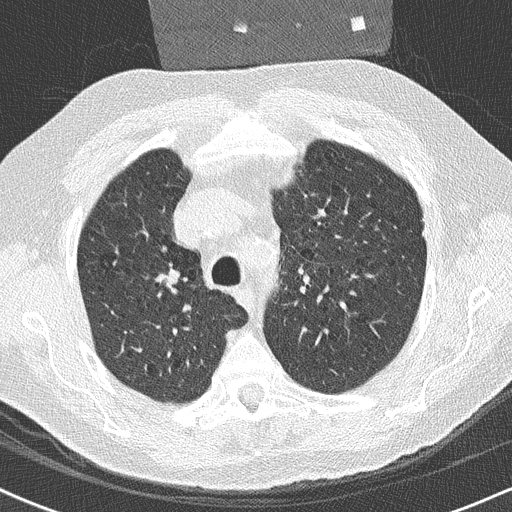
Chest CT (low-dose screening protocol), one axial image; baseline annual screen; lung window (W 1500 / L -600 HU); 2 mm slice thickness; 120 kVp; 512 × 512 image matrix, field of view 314 × 314 mm. Male, age 59 years at enrolment. Former smoker at enrolment.
- Lesion marked by an expert reader, box from (x=145, y=260) to (x=189, y=300) px.
- No non-calcified nodule or mass ≥4 mm was recorded by the screening reader at this exam.
- Official screen result: negative screen, minor abnormalities not suspicious for lung cancer.
- Participant outcome: lung cancer diagnosed 360 days after this screen (after the second annual screen) — squamous cell carcinoma, NOS, right upper lobe, poorly differentiated (G3), stage IIA (AJCC 6th edition), 20 mm at pathology.